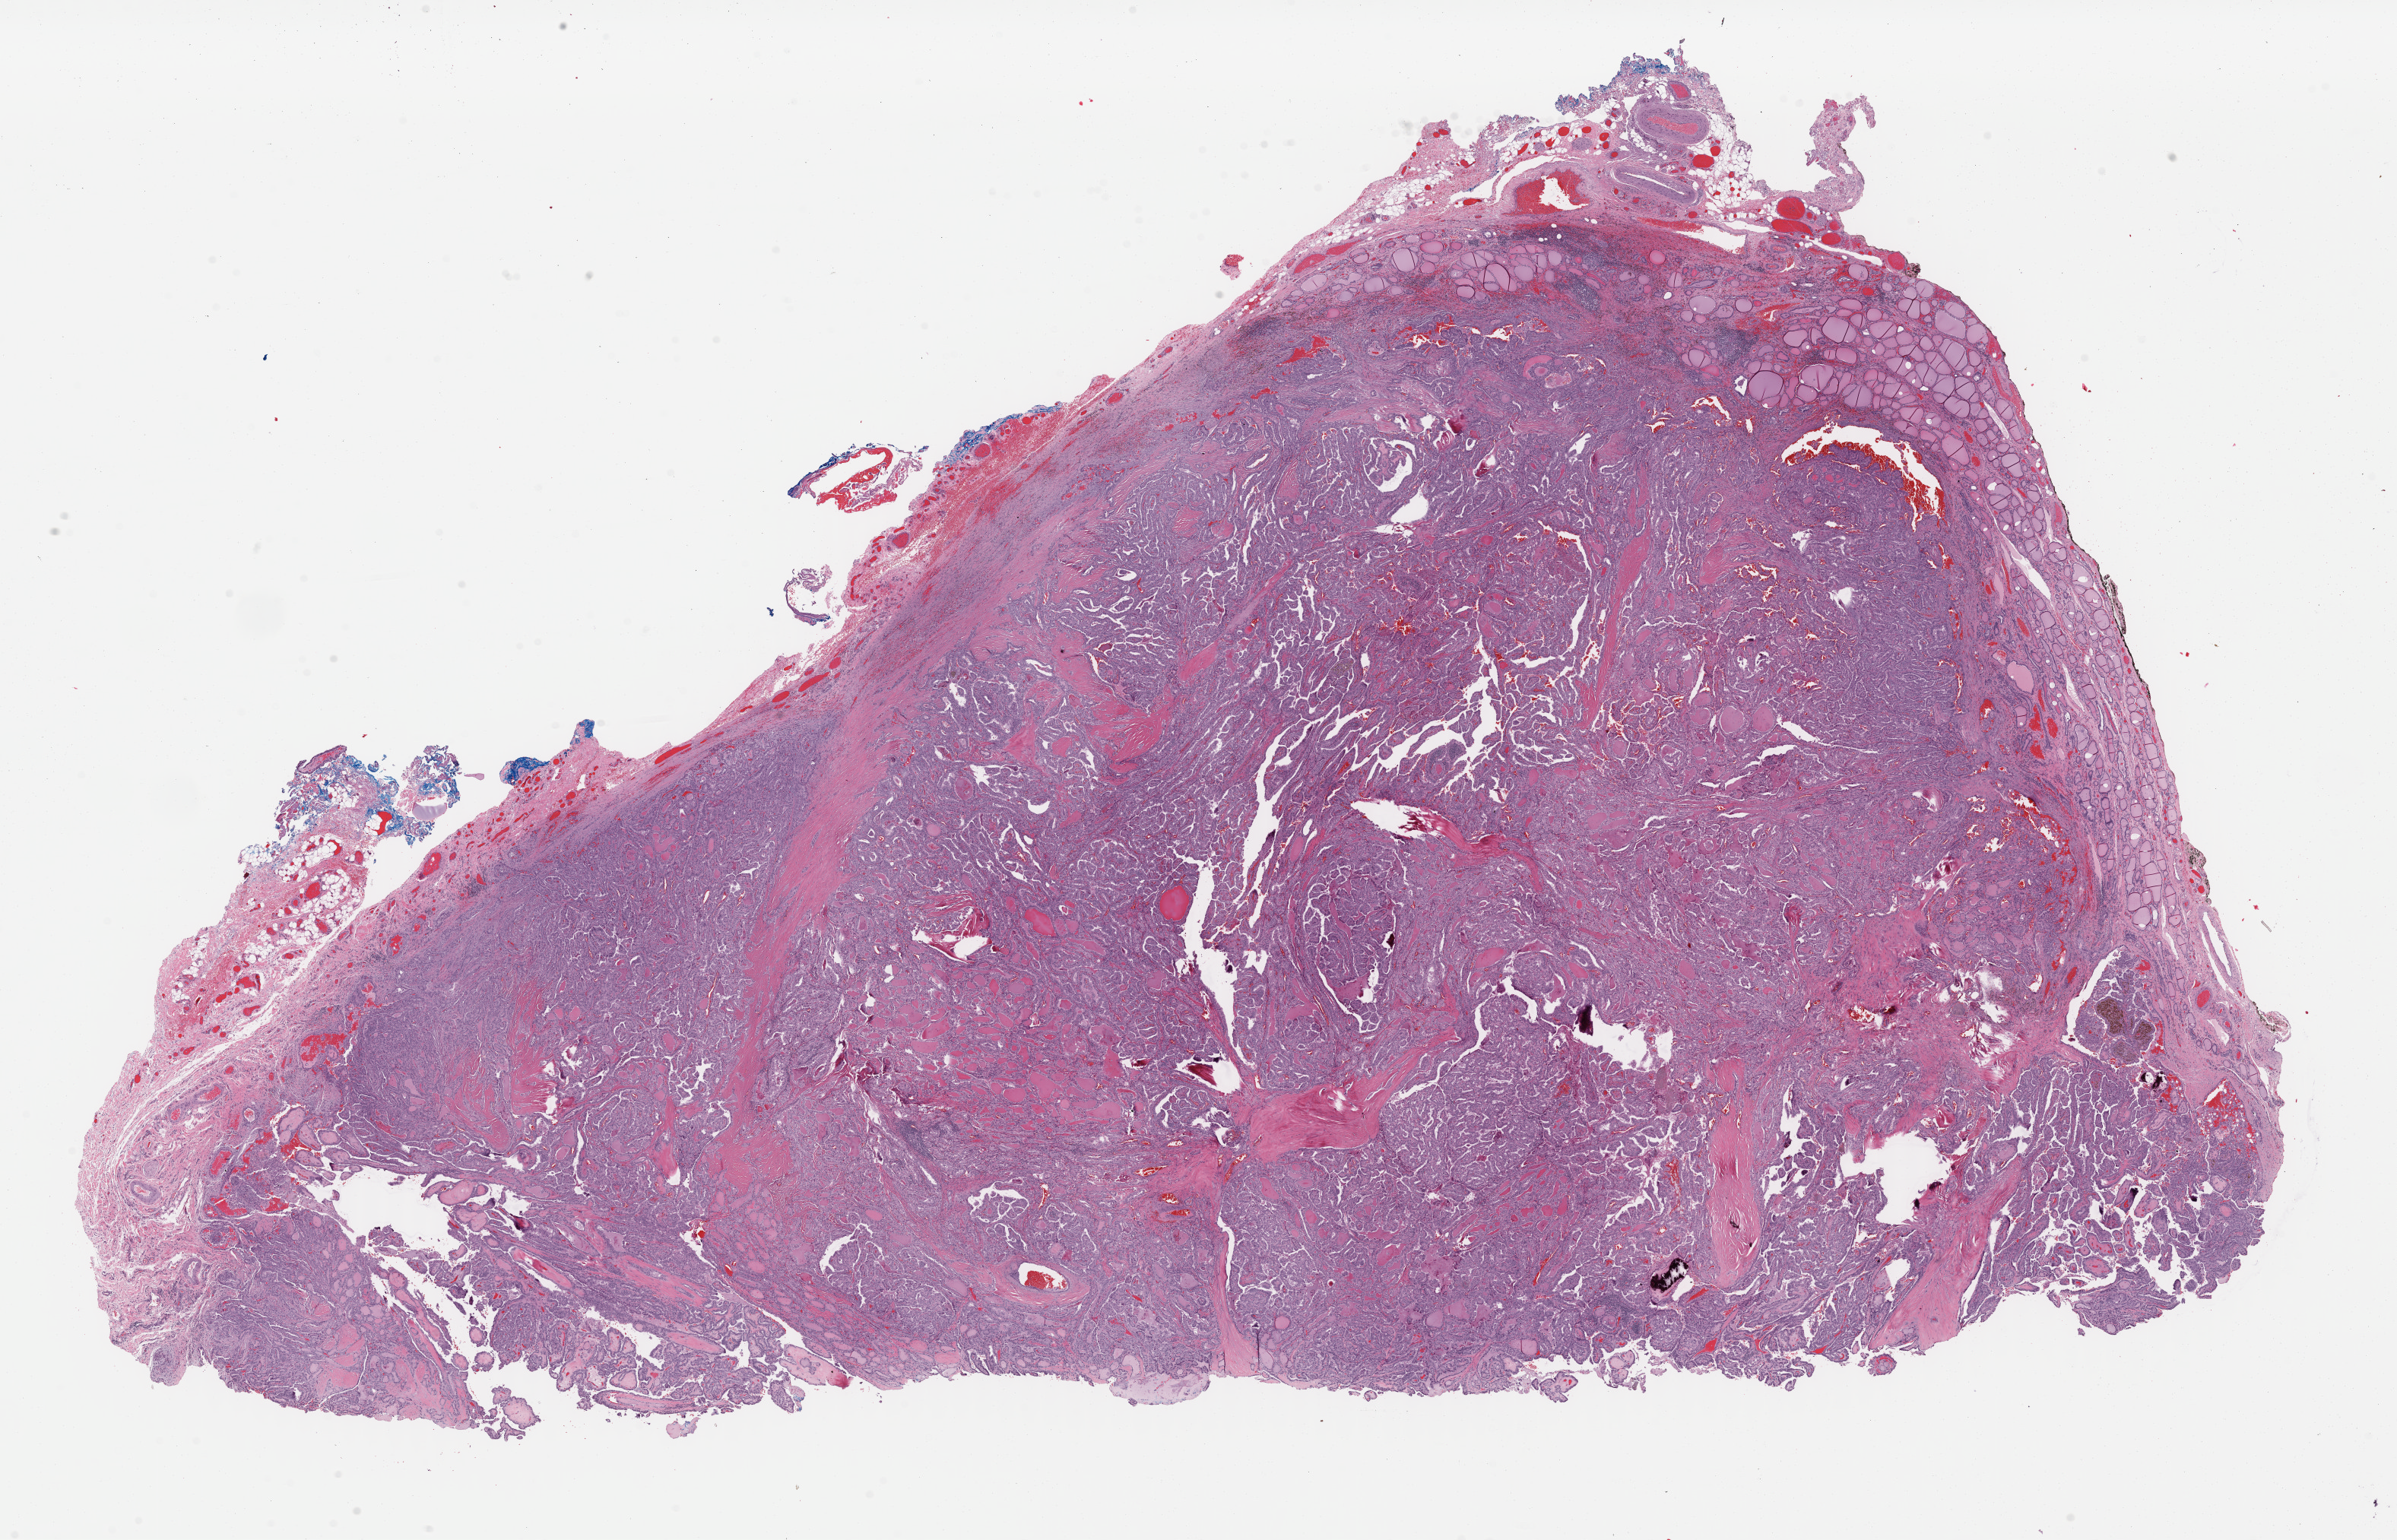
Digitized Hematoxylin and eosin (H&E) stained tissue section (whole slide) — a low-resolution overview of the entire scanned area, about 24.9 x 16.0 mm (from a 40x scan); formalin-fixed paraffin-embedded (FFPE) diagnostic section; primary tumour sample from the thyroid. Male patient; age at initial diagnosis 52 years.
TNM: T3 N1a M0. AJCC pathologic stage: III (7th edition). Lymph nodes positive (case pathology): 1 of 1 examined. Pathologic diagnosis: Papillary carcinoma, columnar cell.